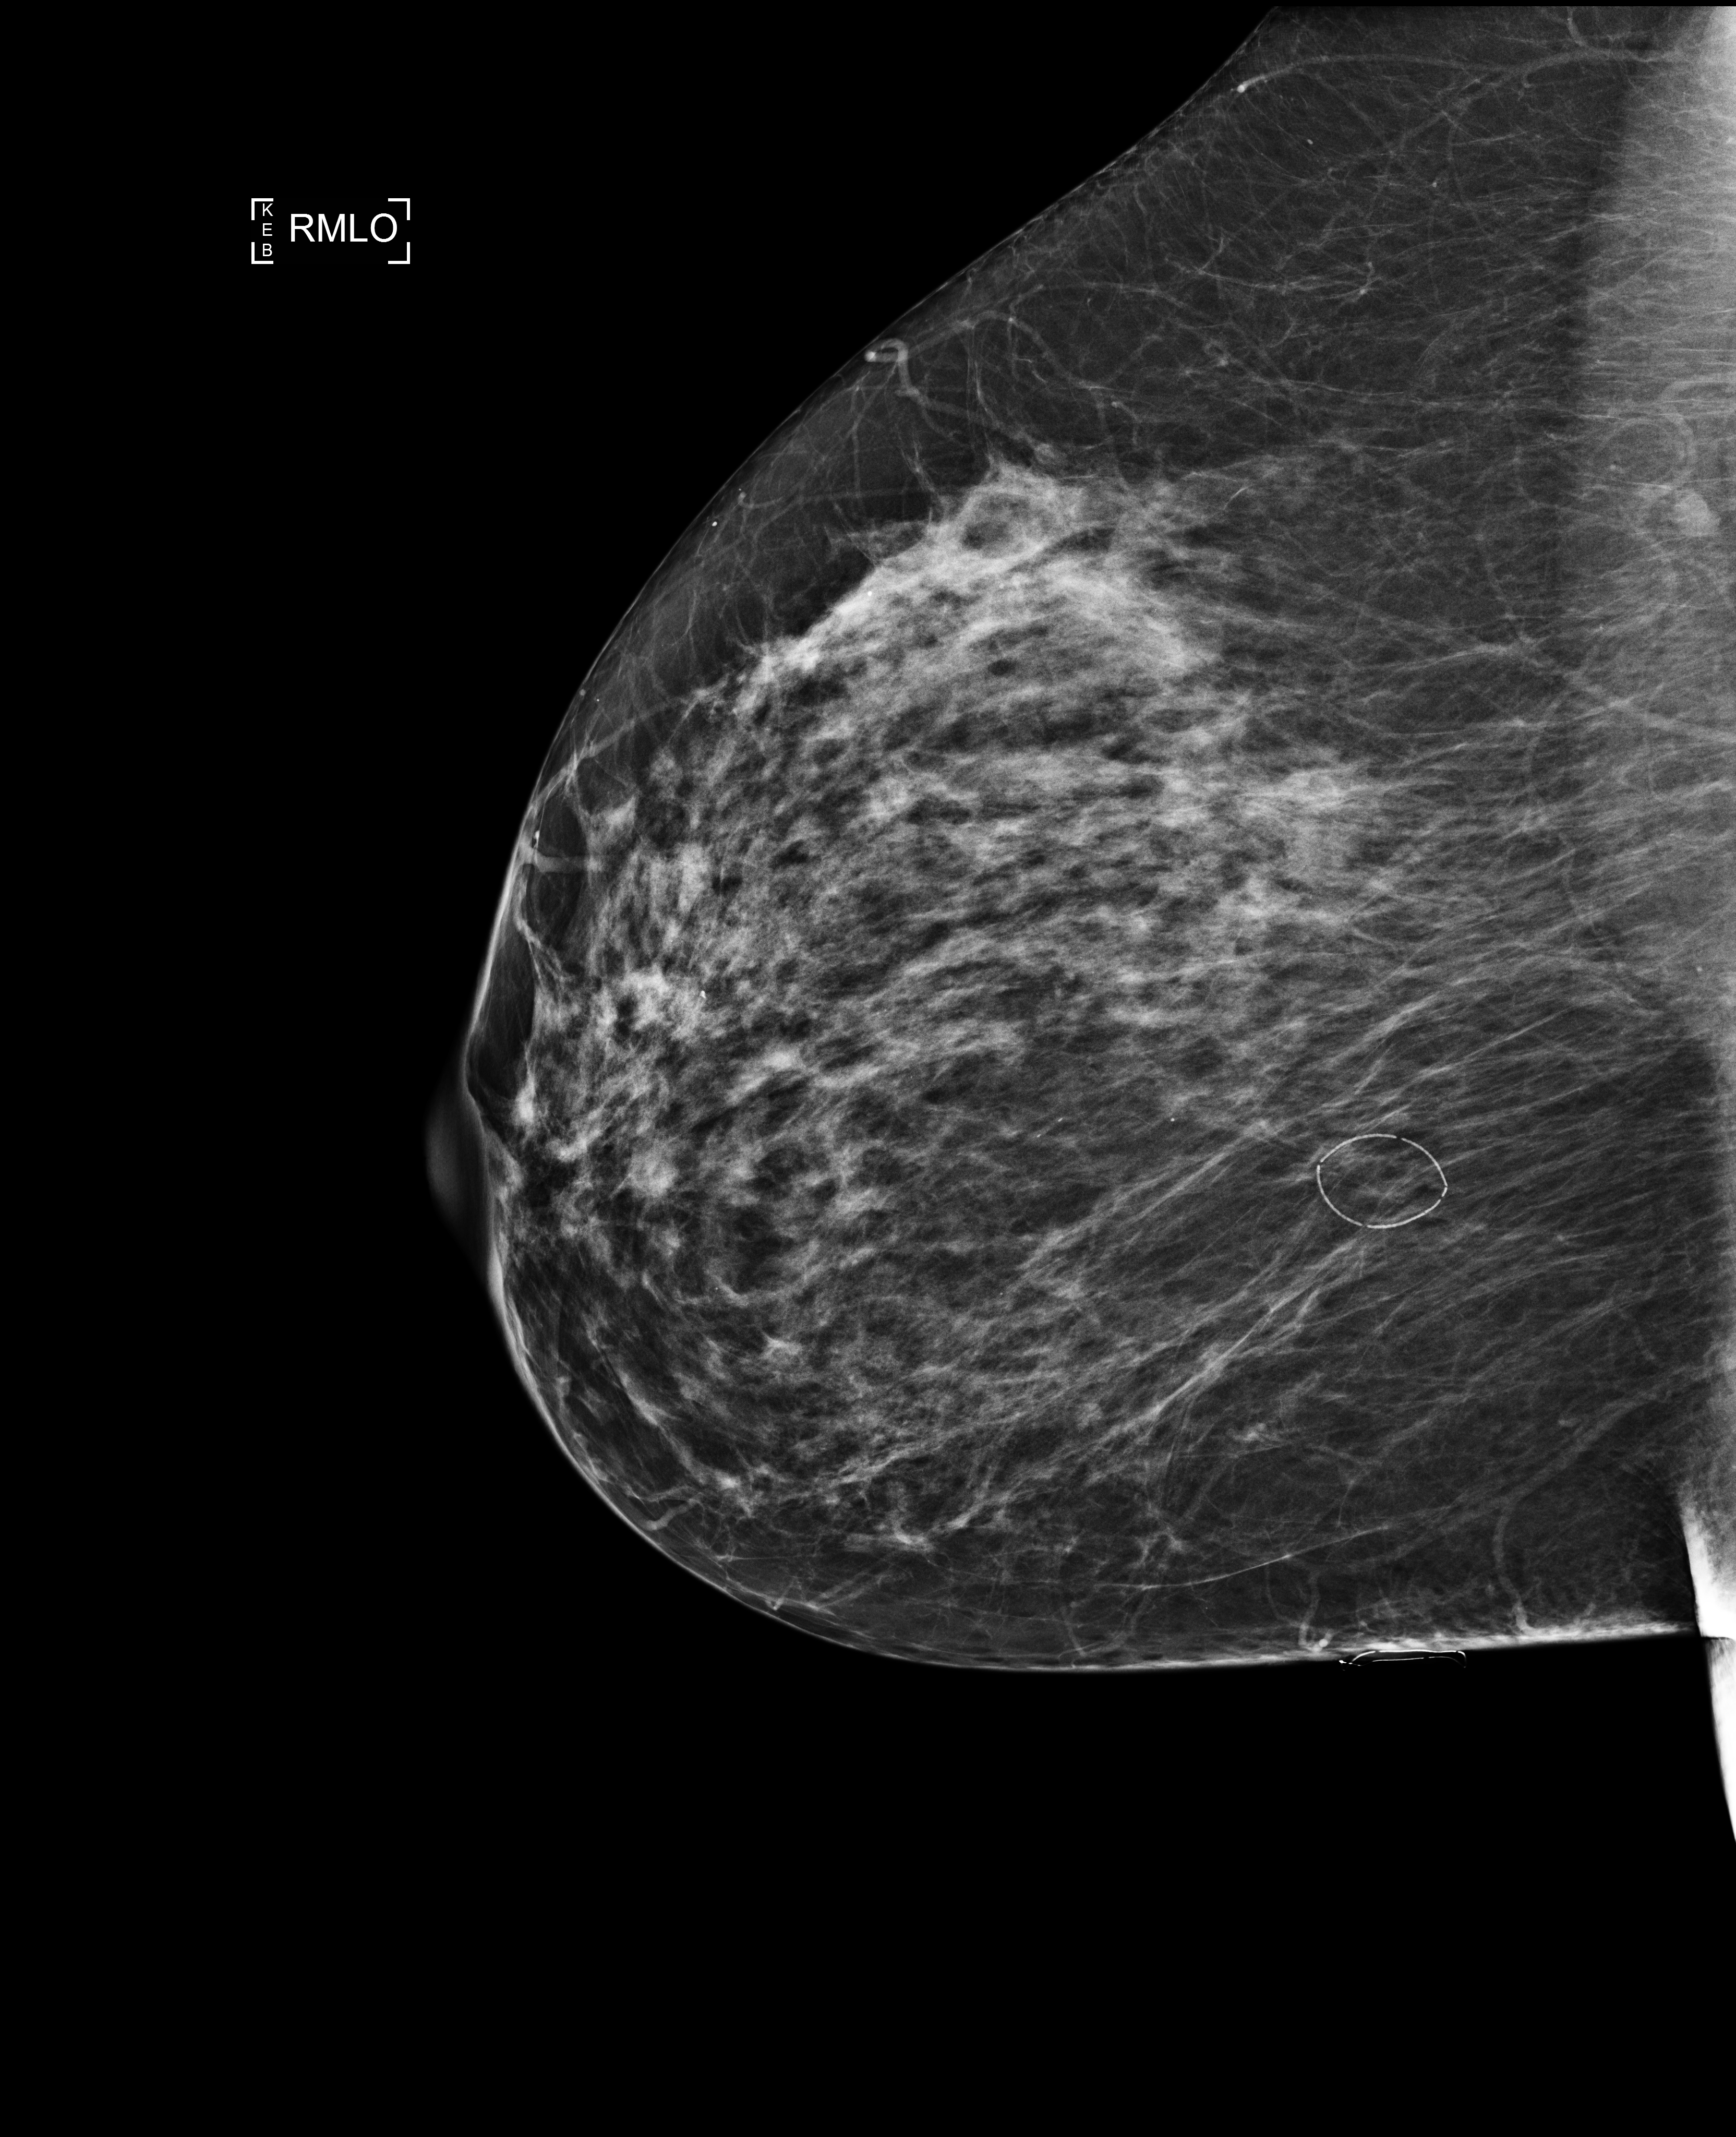
Screening examination; system: Selenia Dimensions. Female patient, age 62 years.
Image type: full-field digital mammogram. Breast: right. Projection: medio-lateral oblique projection.